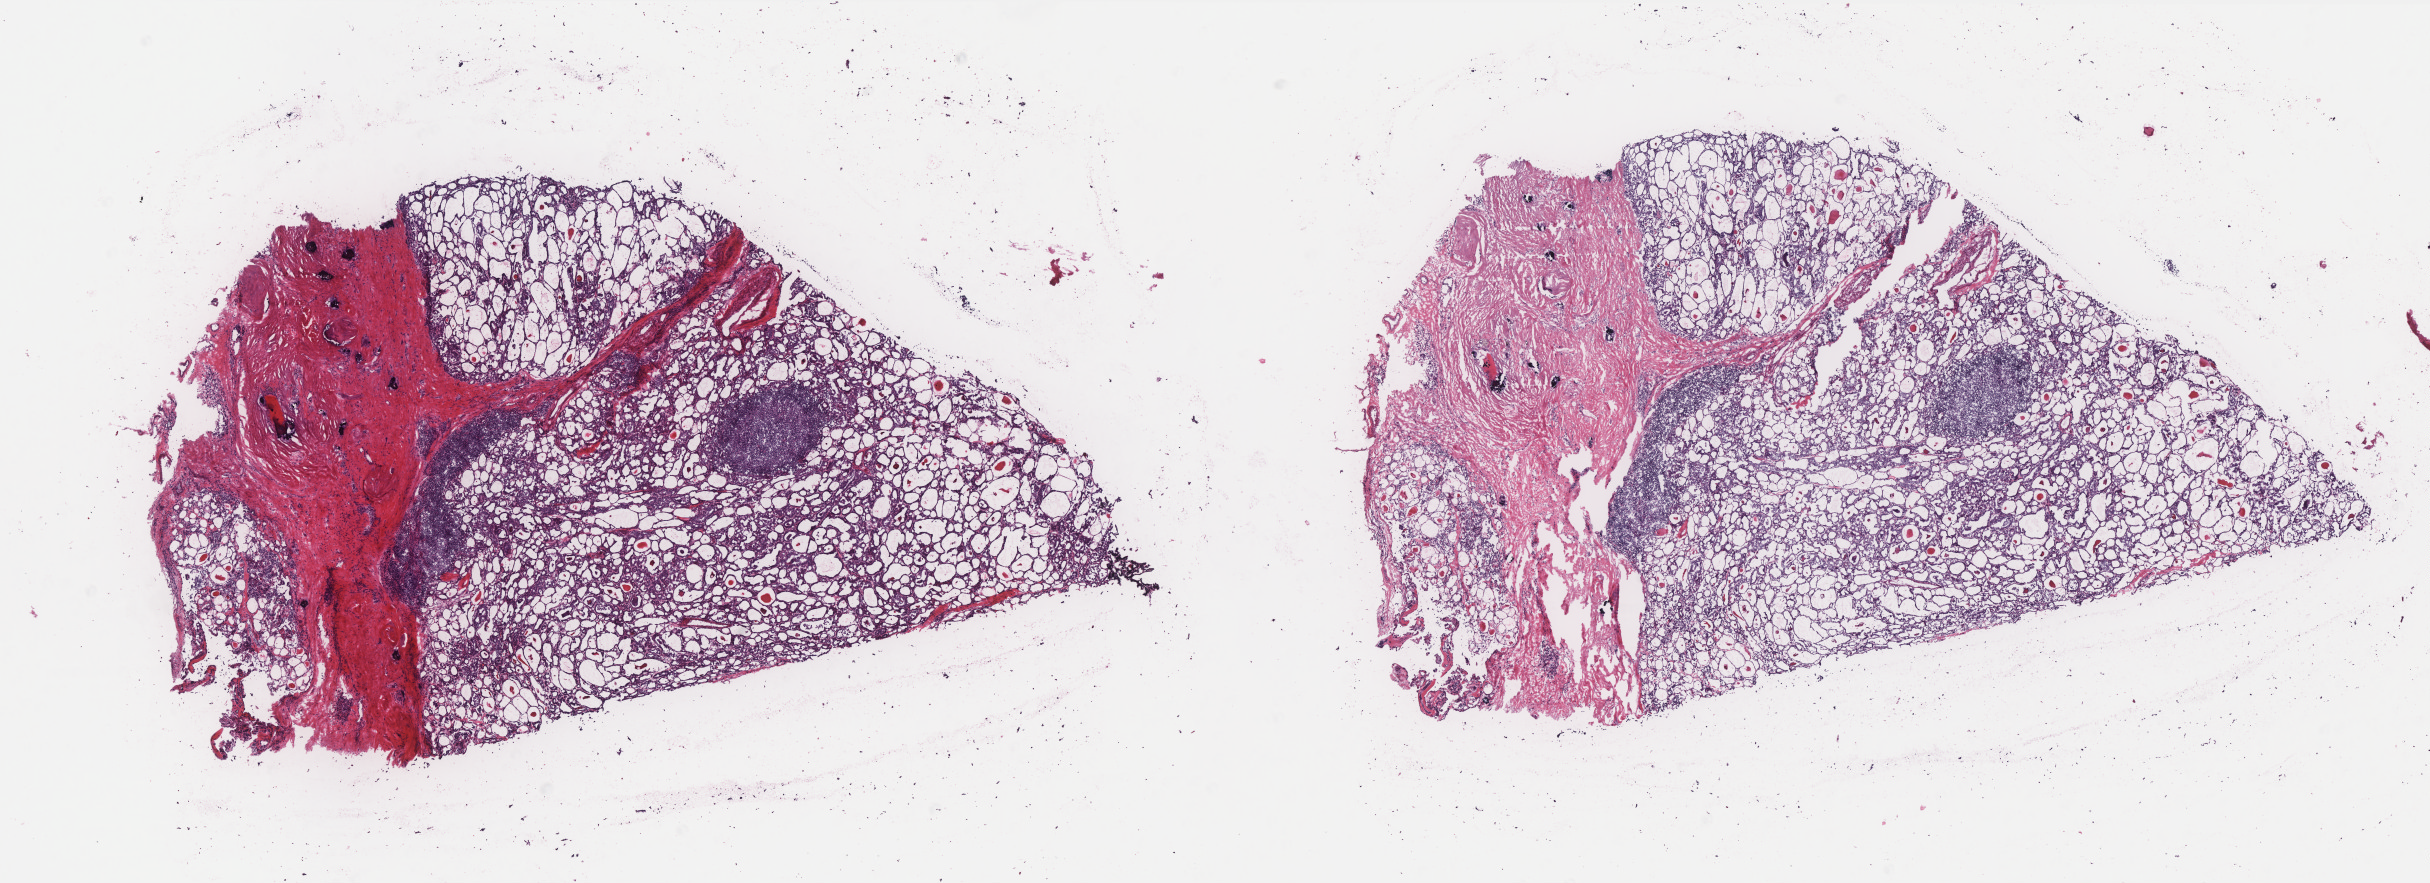
Whole-slide histology image, H&E — whole scanned area (about 19.5 x 7.1 mm, from a 40x scan) shown as a low-resolution overview; frozen section from the top of the tissue portion; sample: primary tumour, thyroid. Male patient; age at initial diagnosis 36 years. Pathologist review of this section (percent, as recorded): tumour cells 80%, tumour nuclei 80%.
Pathologic diagnosis: Papillary adenocarcinoma, NOS (thyroid gland).